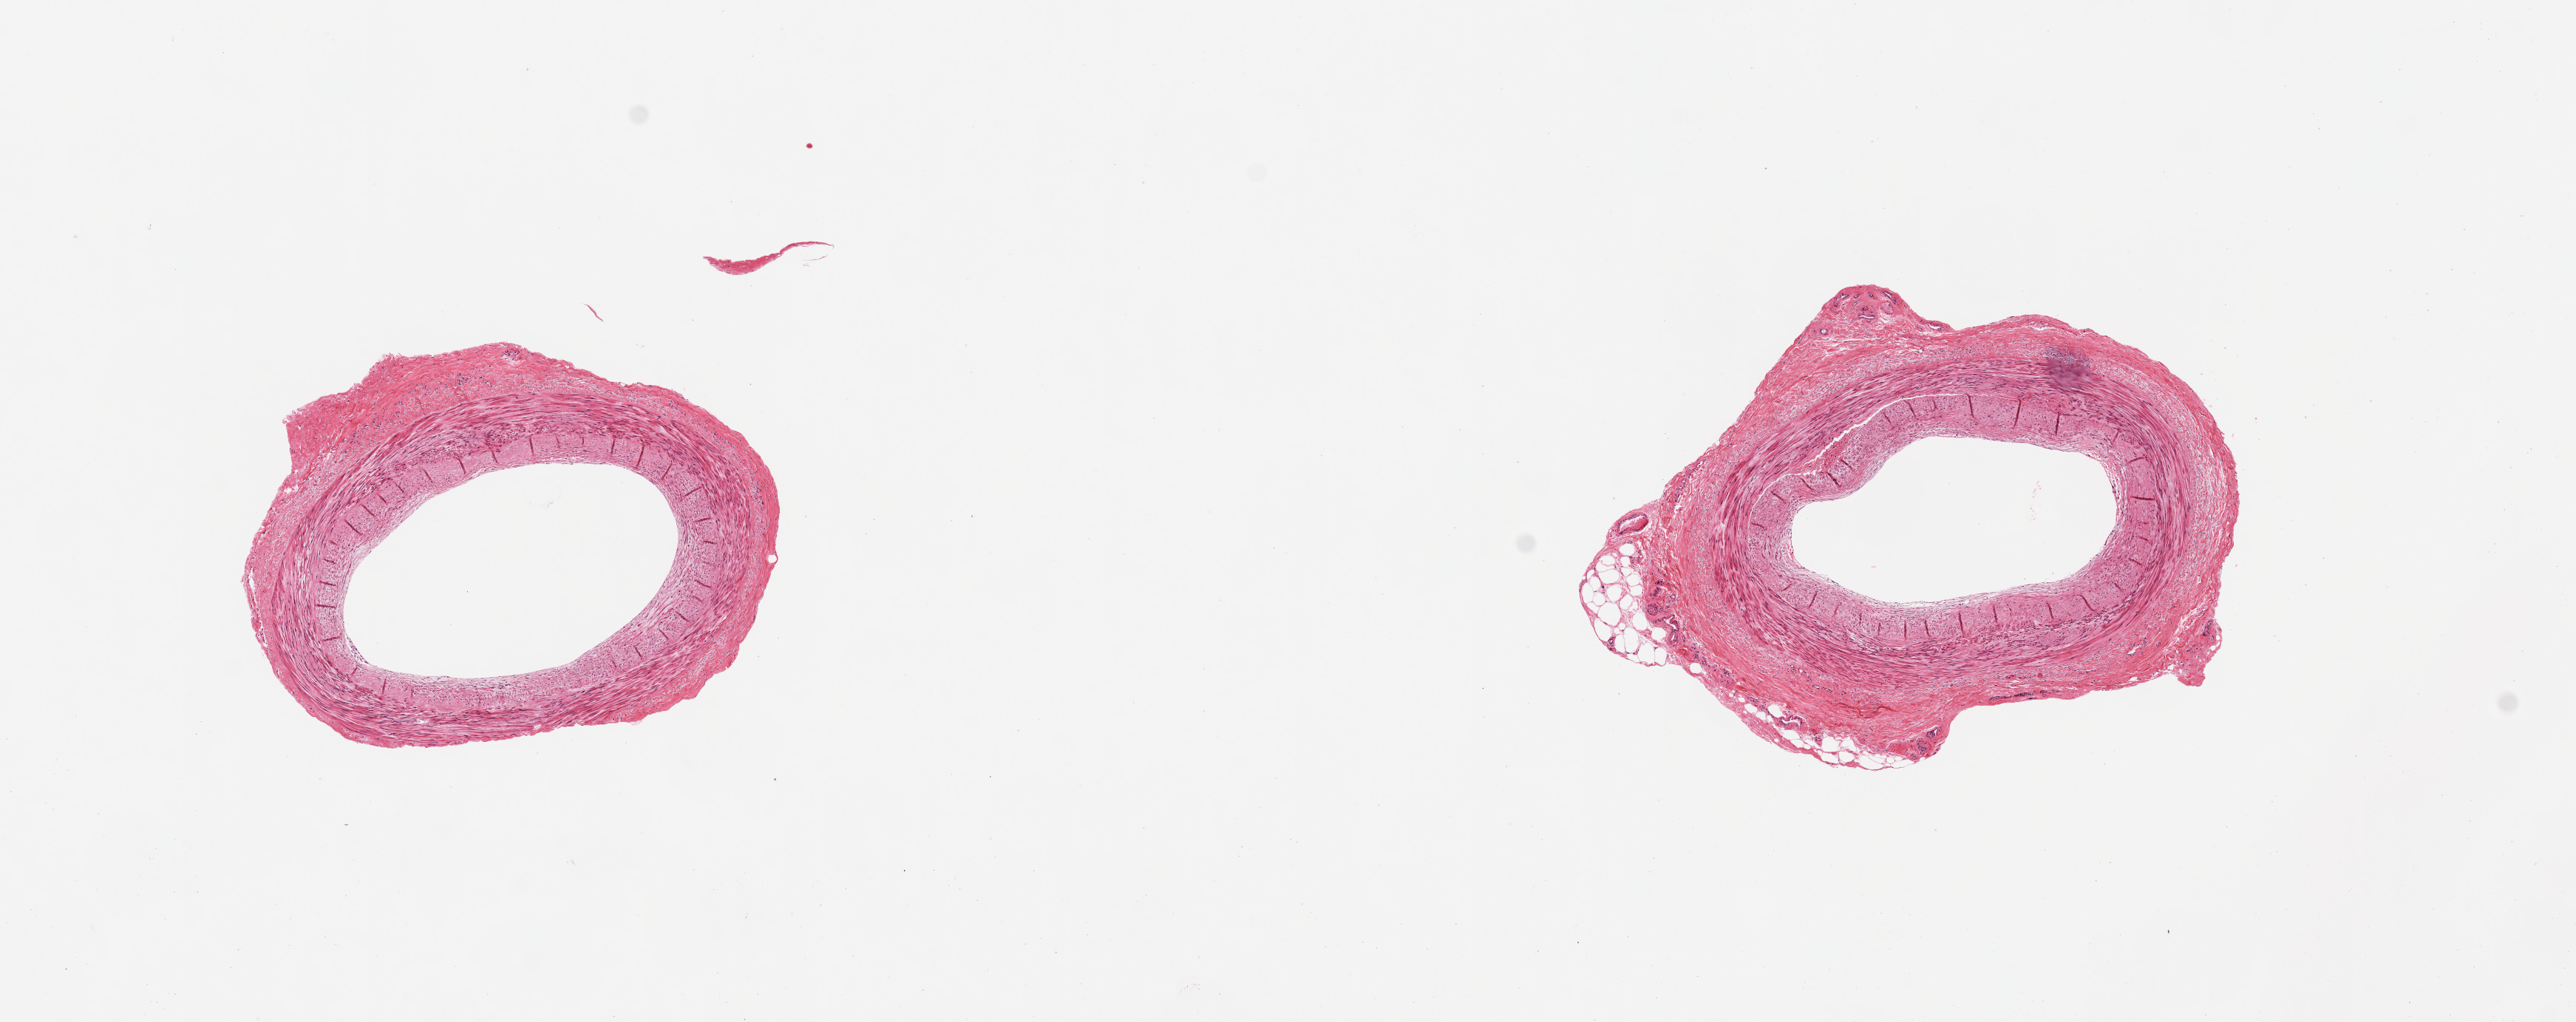
Haematoxylin and eosin whole-slide image, brightfield, a low-resolution overview of the entire scanned area, about 13.8 x 5.5 mm; PAXgene-fixed paraffin-embedded (PFPE) section; section of tibial artery (target tissue); donor tissue sample. Donor sex: female.
Pathologist's review note for this sample: 2 pieces, trace adherent fat; good specimens.